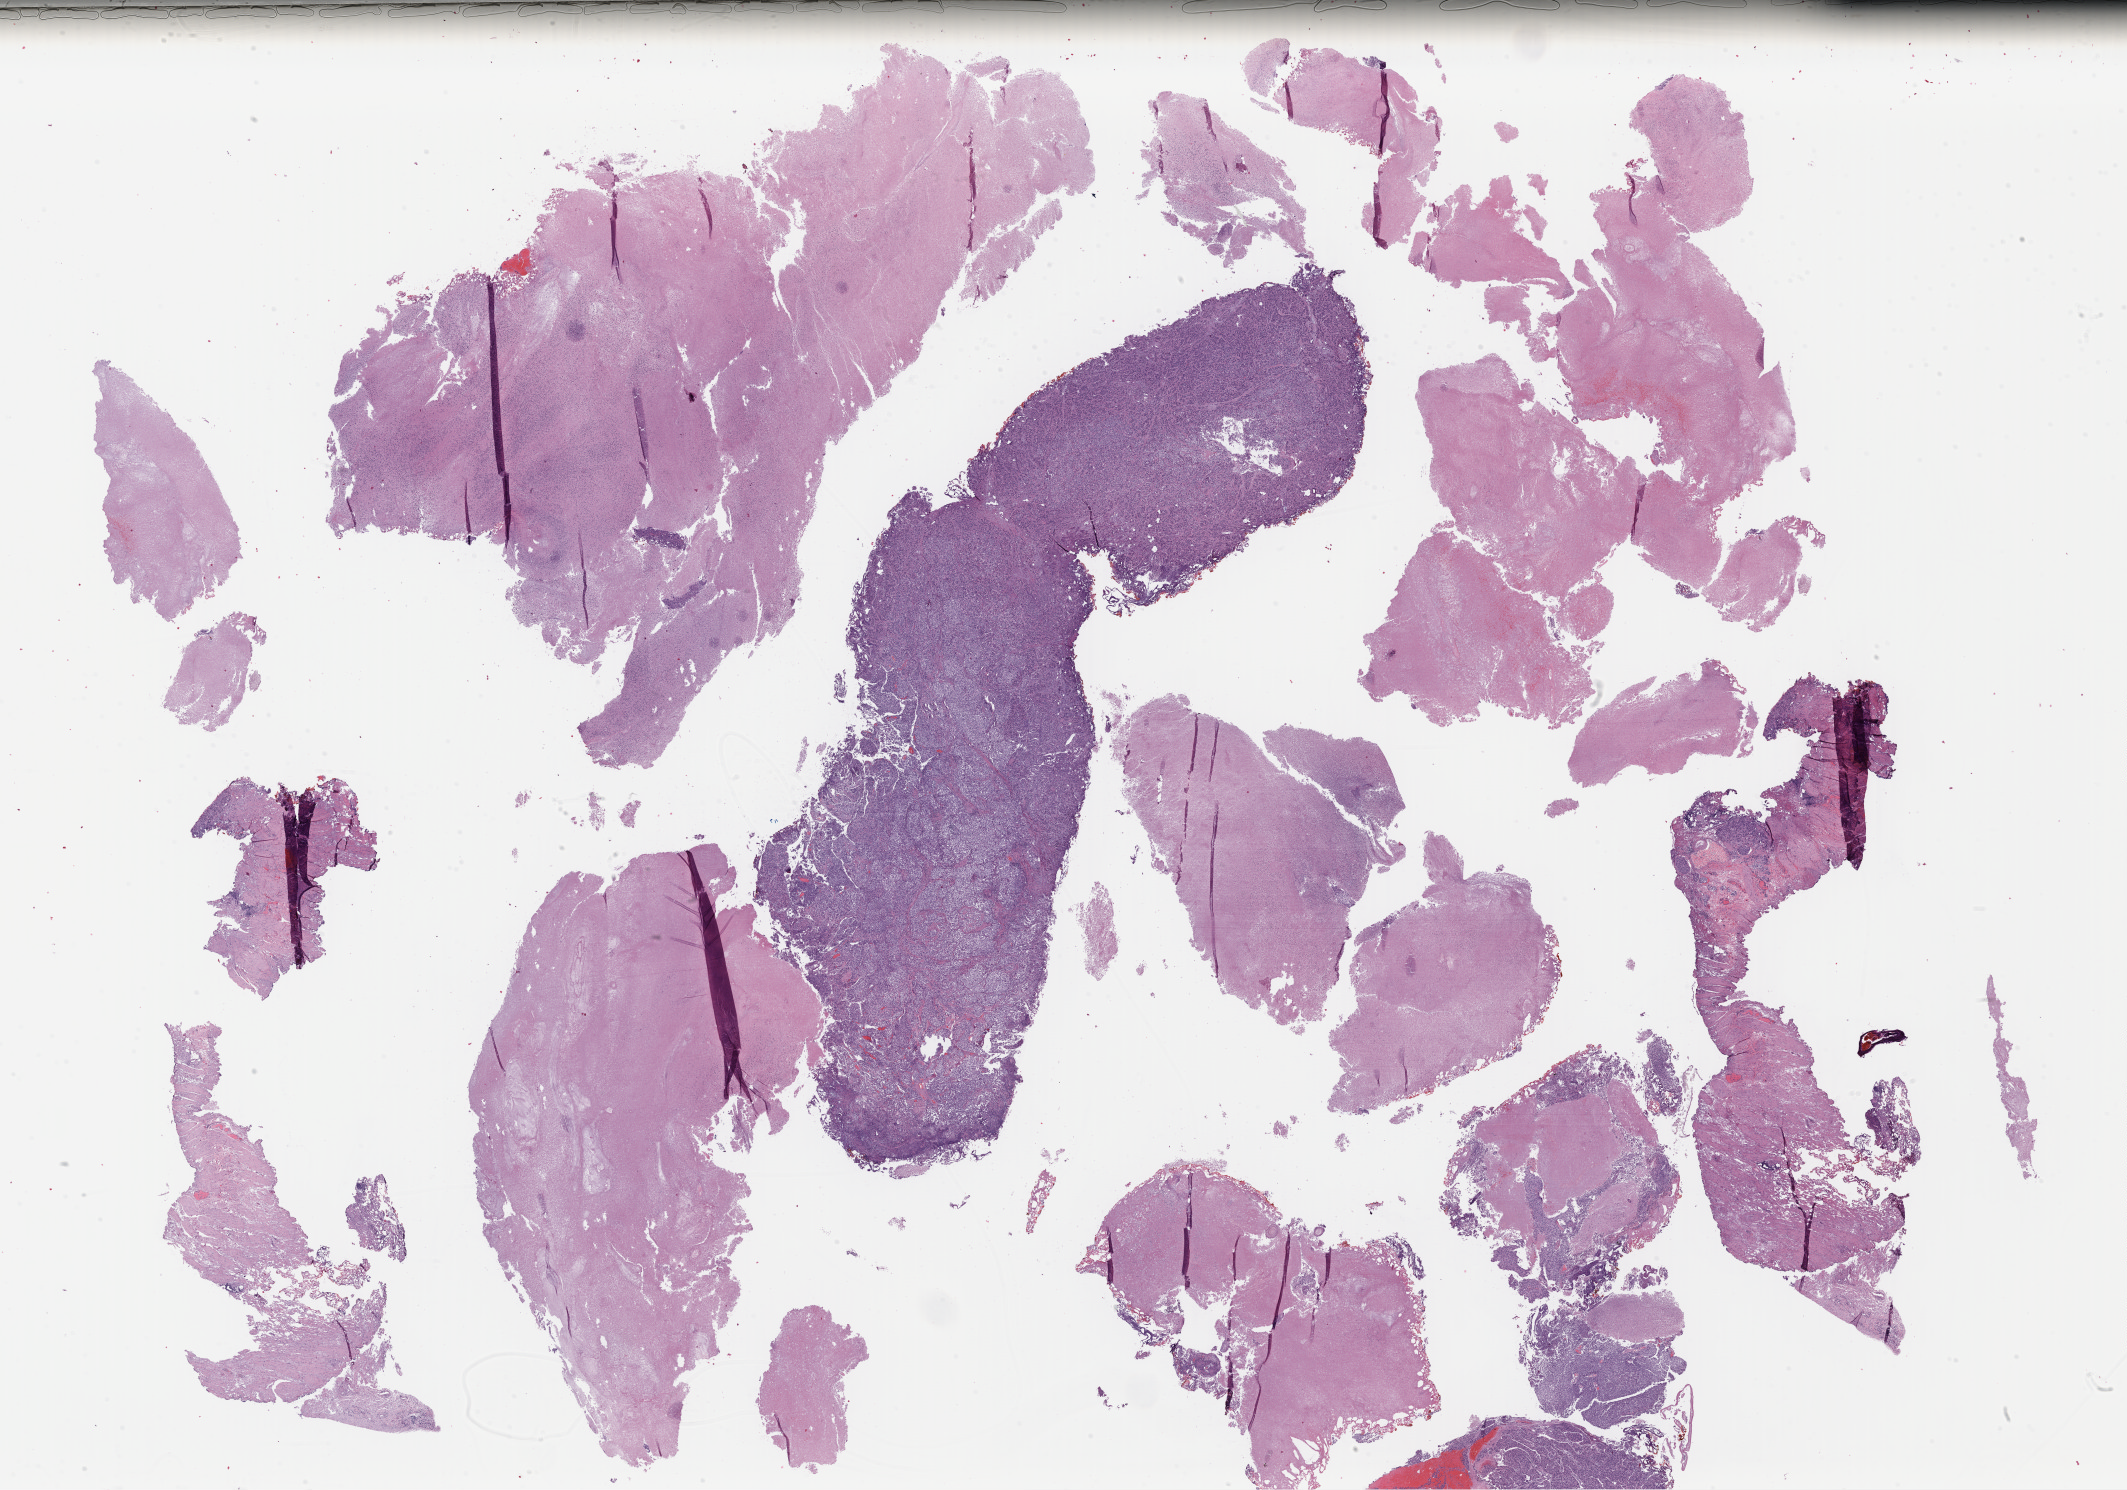
Digitized H&E tissue section (whole slide), low-resolution overview of the scanned area, about 33.4 x 23.4 mm (slide scanned at 40x); formalin-fixed paraffin-embedded (FFPE) diagnostic section; sample: primary tumour, bladder. Male, age 65 years at initial diagnosis.
Histologic diagnosis: Transitional cell carcinoma.